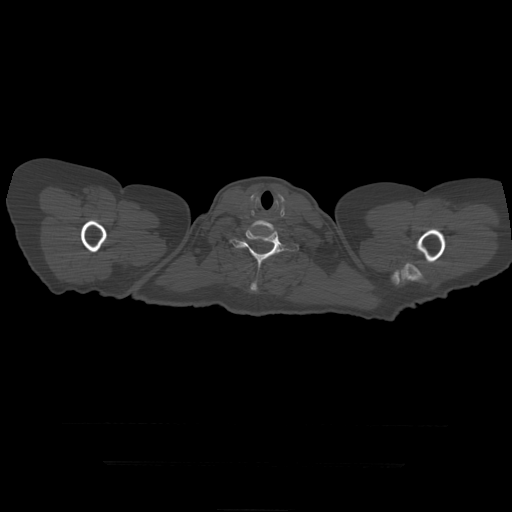
CT including the spine, one axial slice. Slice 391 of 399 in the series (ordered by position). Reconstruction kernel STANDARD. 120 kVp. Bone window (W 1800 / L 400 HU). 1.25 mm slice thickness. 512 × 512 image matrix, field of view 450 × 450 mm. Patient age 41 years. From the clinical record (not read from this slice): primary cancer: breast.
Annotated regions visible in this slice (semi-automatic segmentation, software-assisted and operator-edited):
- T1 vertebra: box from (x=230, y=230) to (x=299, y=291) px